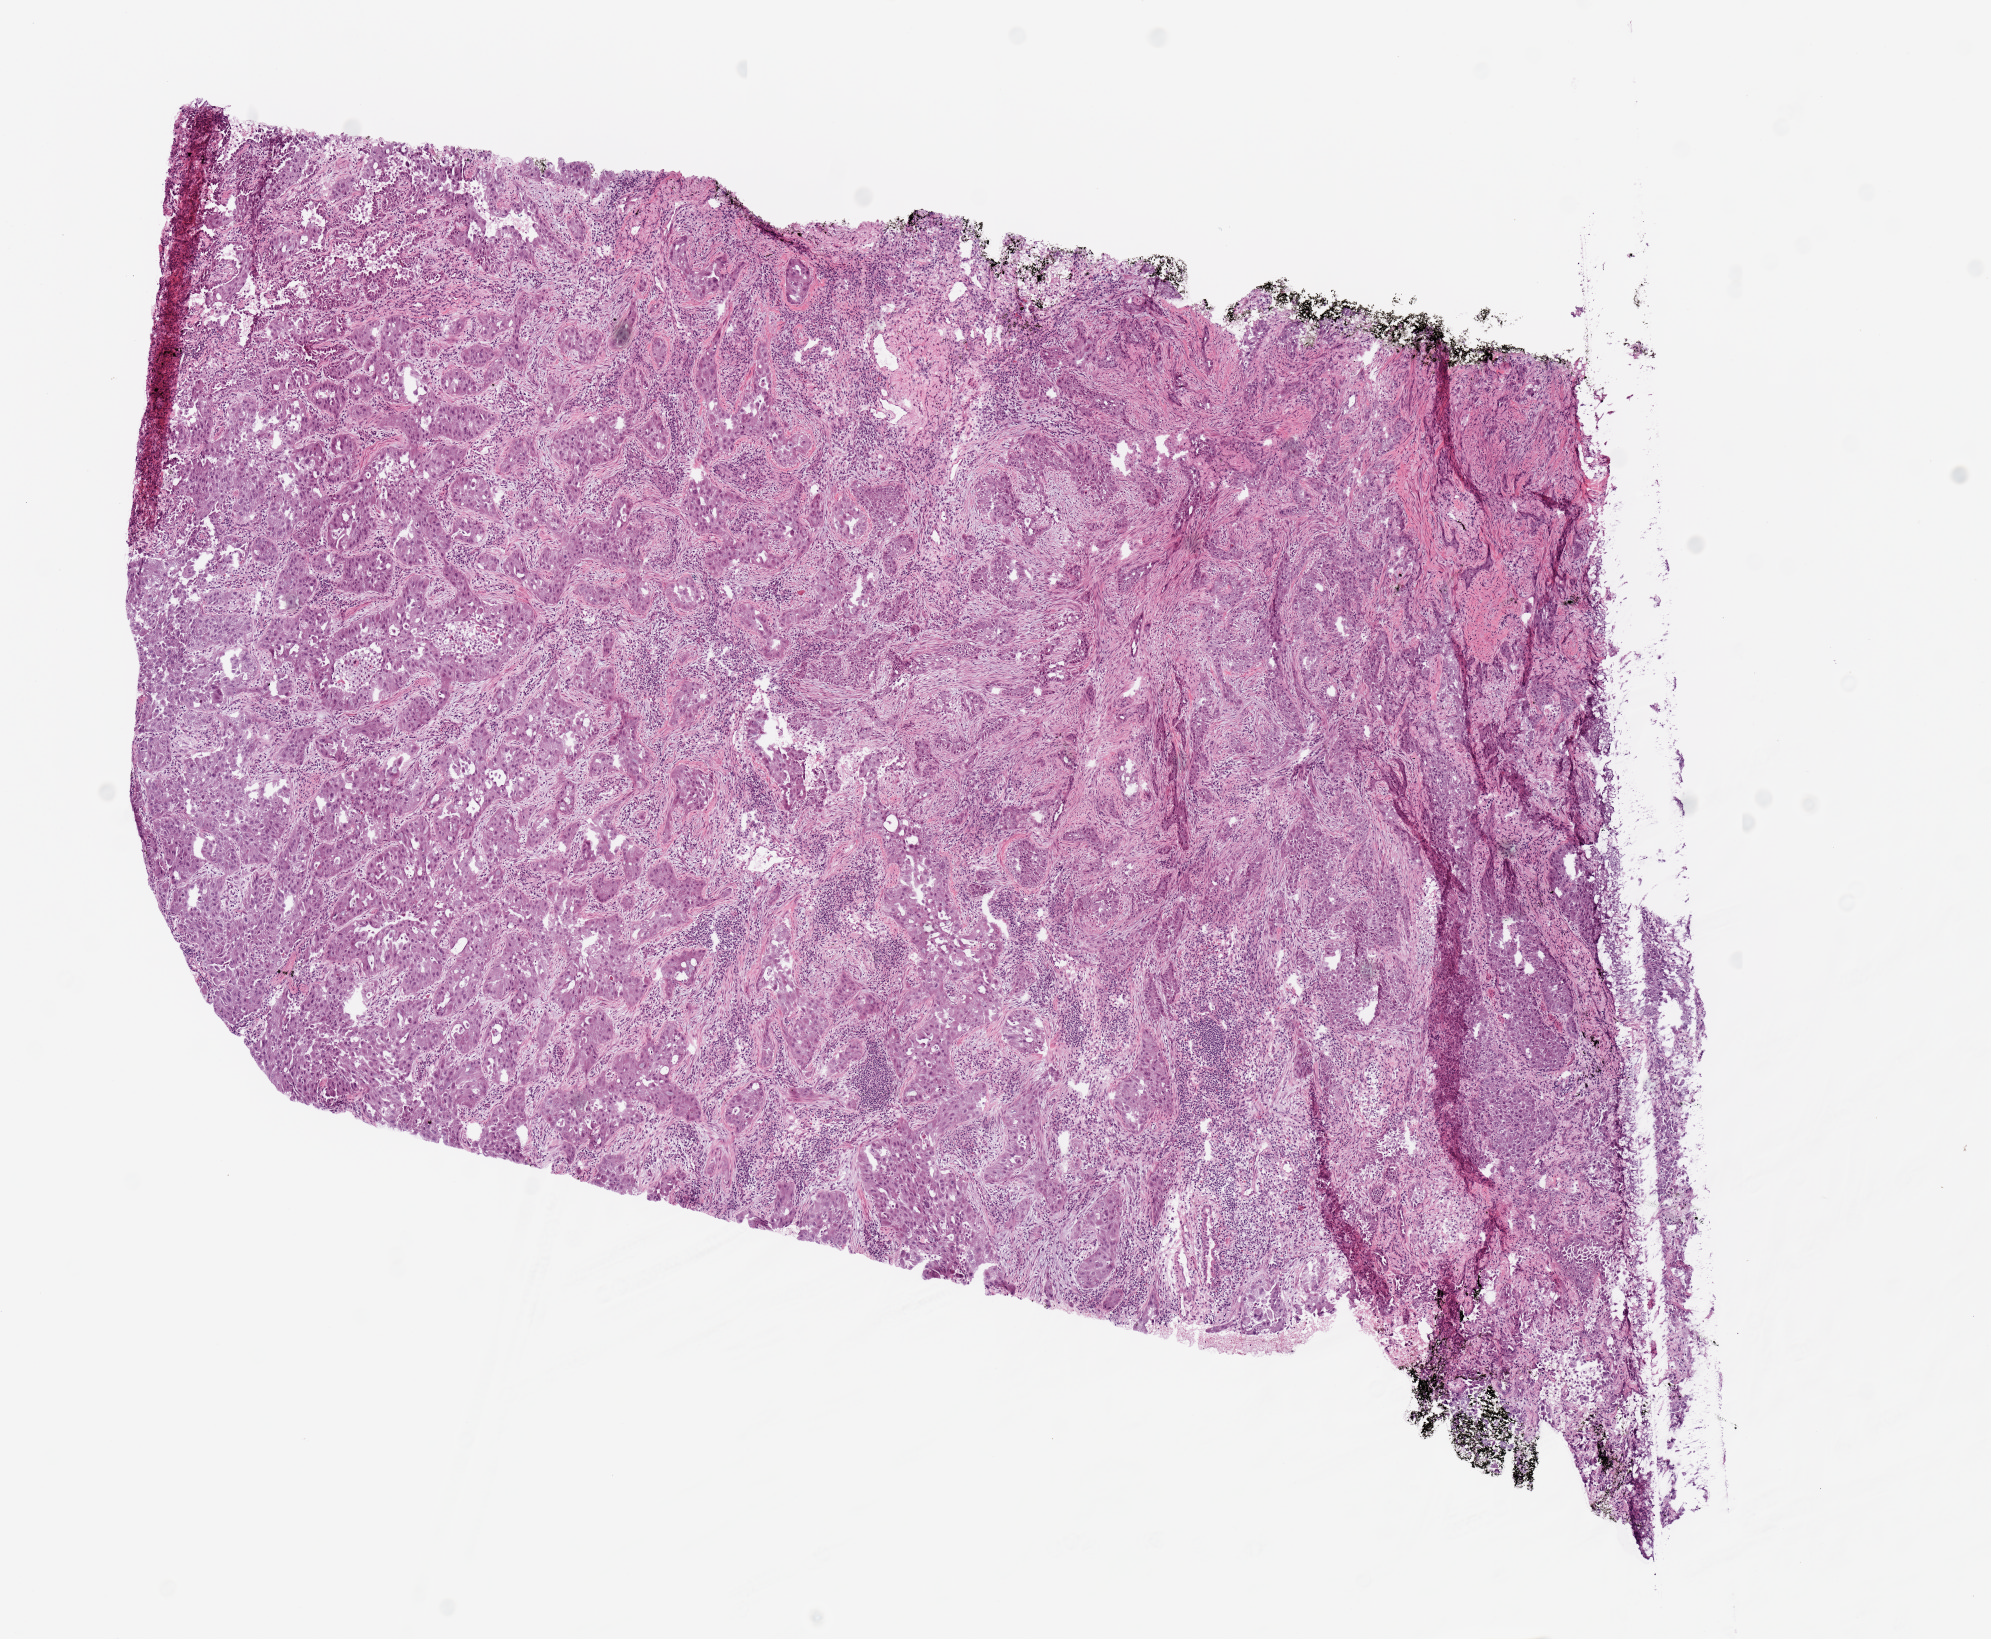
Digitized Hematoxylin and eosin (H&E) stained tissue section (whole slide), whole scanned area (about 7.9 x 6.5 mm) shown as a low-resolution overview, frozen section from the top of the tissue portion, sample: primary tumour, lung. Patient: female, age at initial diagnosis 53 years. Composition of this section per pathologist review: tumour cells 100%, tumour nuclei 72%, normal cells 0%, stromal cells 0%, necrosis 0%. Infiltration values recorded for this section: lymphocyte infiltration 16%, monocyte infiltration 0%, neutrophil infiltration 0%.
Histologic diagnosis: Adenocarcinoma, NOS (upper lobe, lung). TNM: T1 N2 M0. AJCC pathologic stage: IIIA (6th edition).